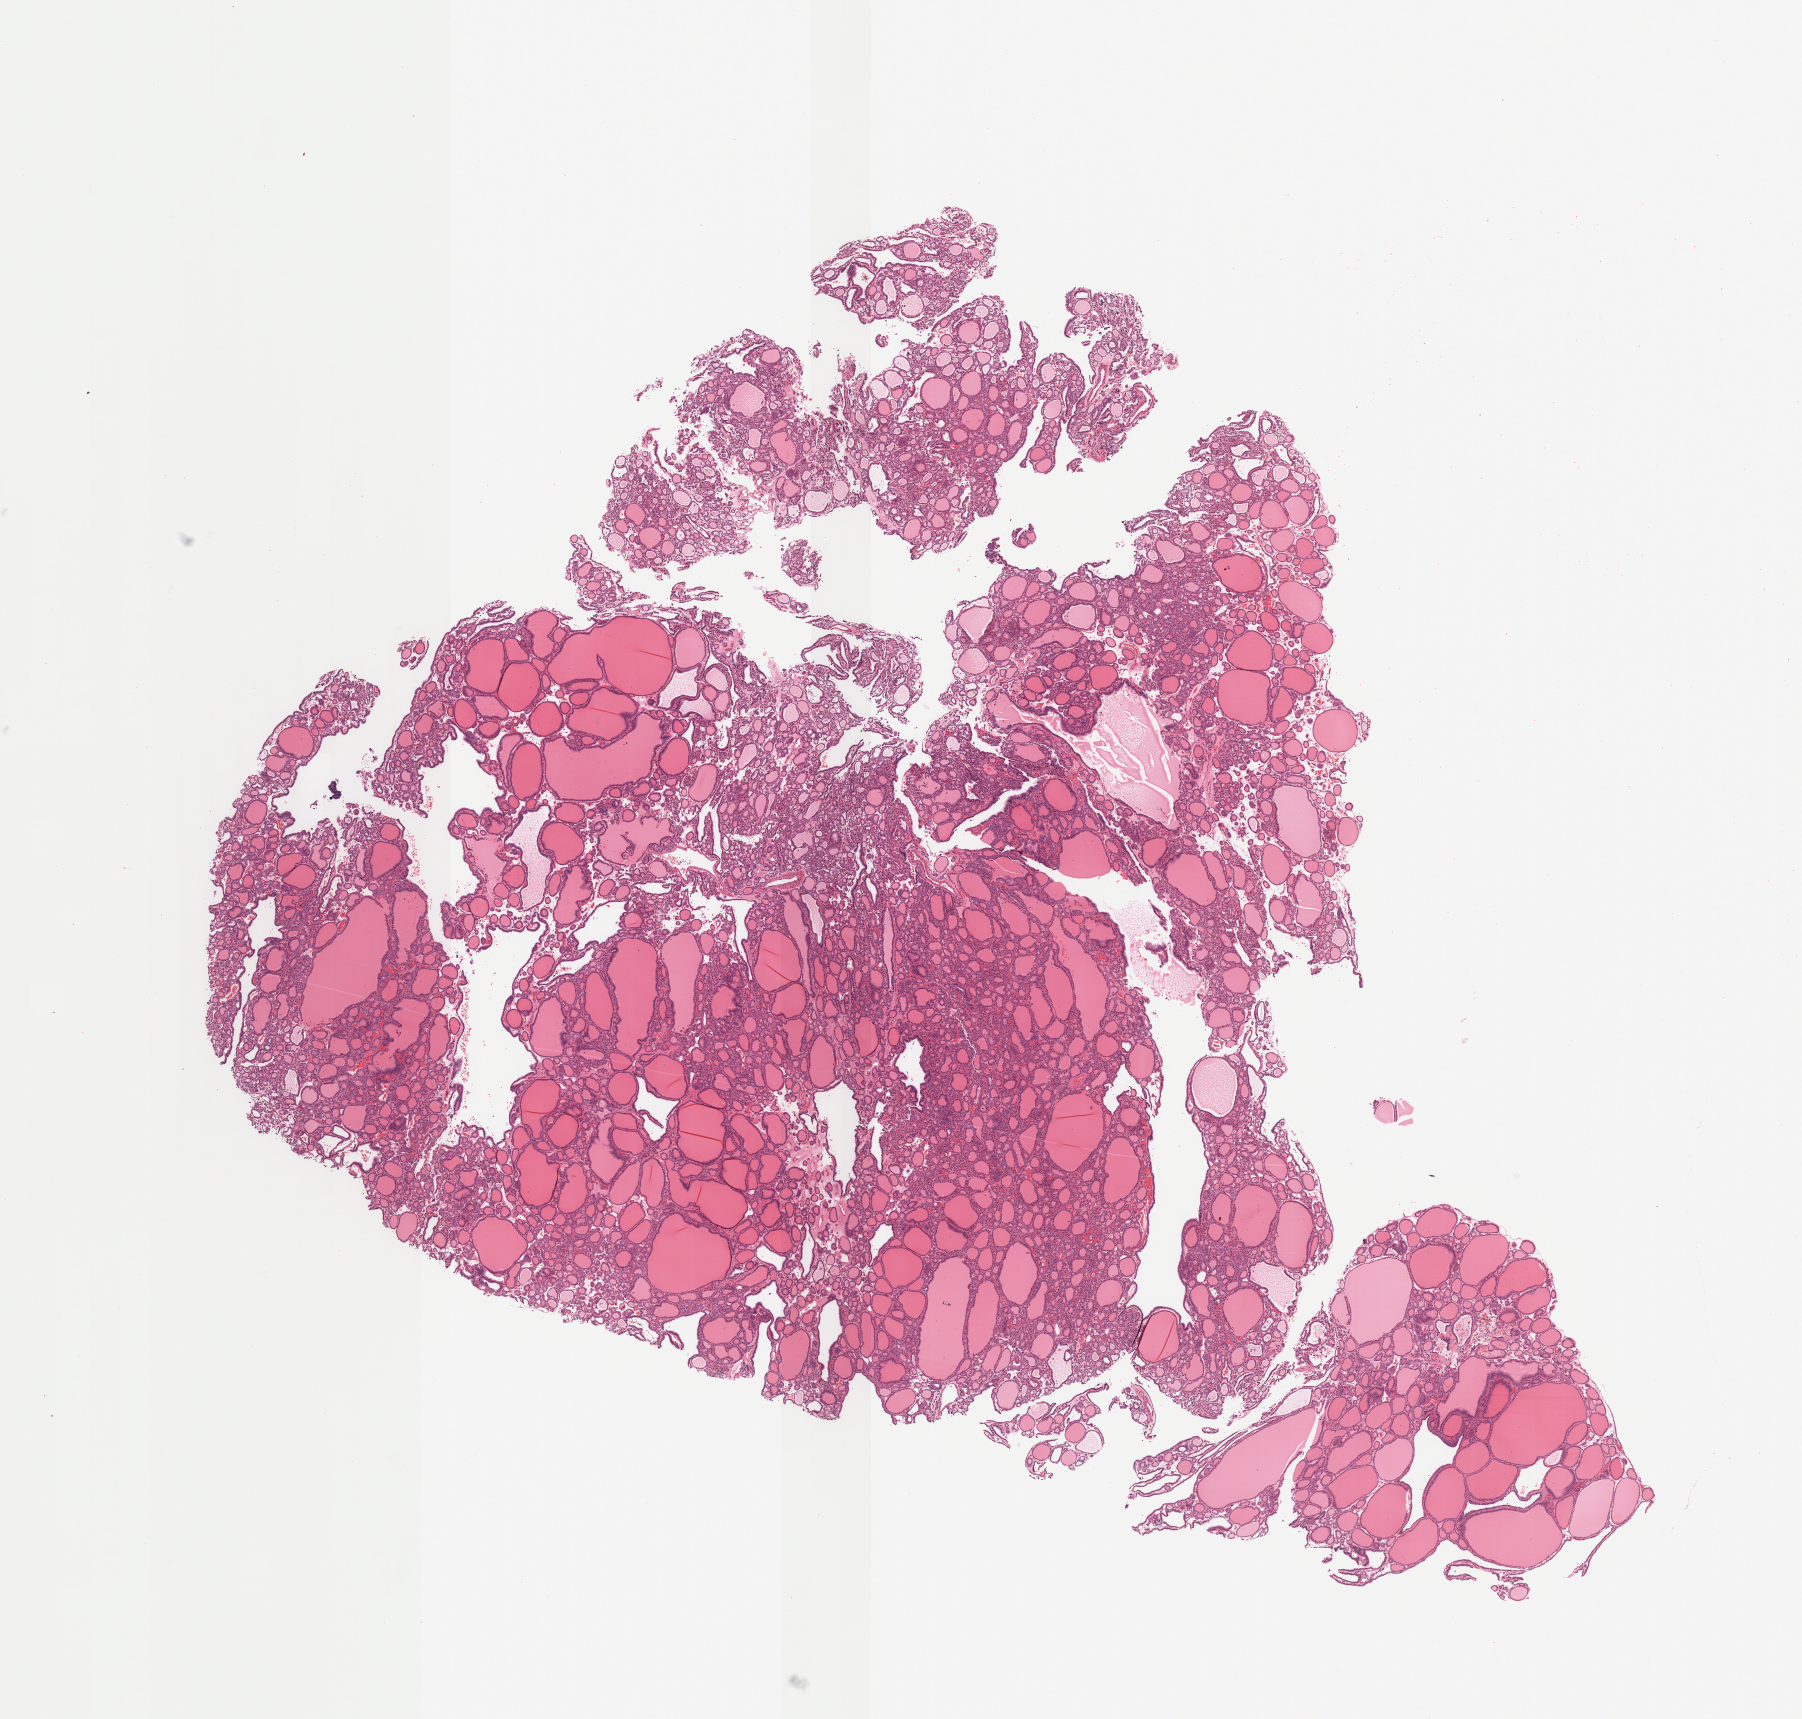
H&E-stained whole-slide image — shown as a low-resolution overview of the whole scanned area (about 14.5 x 13.8 mm, slide scanned at 40x); FFPE section; primary tumour sample from the thyroid. Male patient; age at initial diagnosis 31 years.
Laterality: left. AJCC pathologic stage: I (7th edition). TNM: T2 NX MX. Histologic diagnosis: Papillary carcinoma, follicular variant (thyroid gland).